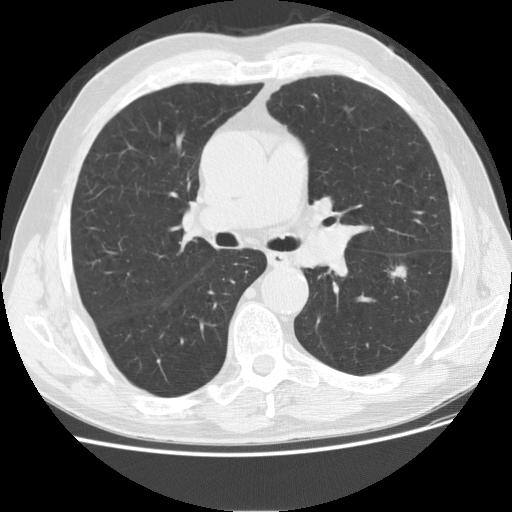
Chest CT (low-dose screening protocol), one axial image; second annual screen; lung window (W 1500 / L -600 HU); 2.5 mm slice thickness; standard (soft-tissue) reconstruction kernel (STANDARD). Male participant, aged 73 years at enrolment. Current smoker at enrolment.
Lesion marked by an expert reader, box from (x=364, y=252) to (x=426, y=304) px. Screening reader's record for this exam (one nodule recorded; not confirmed to be the boxed lesion): non-calcified nodule or mass ≥4 mm, left lower lobe, 16 × 10 mm, smooth margins, soft tissue attenuation, pre-existing on the prior screen: yes; interval growth: yes. Official screen result: positive, other. Lung cancer was diagnosed 76 days after this screen: adenocarcinoma, NOS, left lower lobe, poorly differentiated (G3), stage IIA (AJCC 6th edition), 12 mm at pathology.